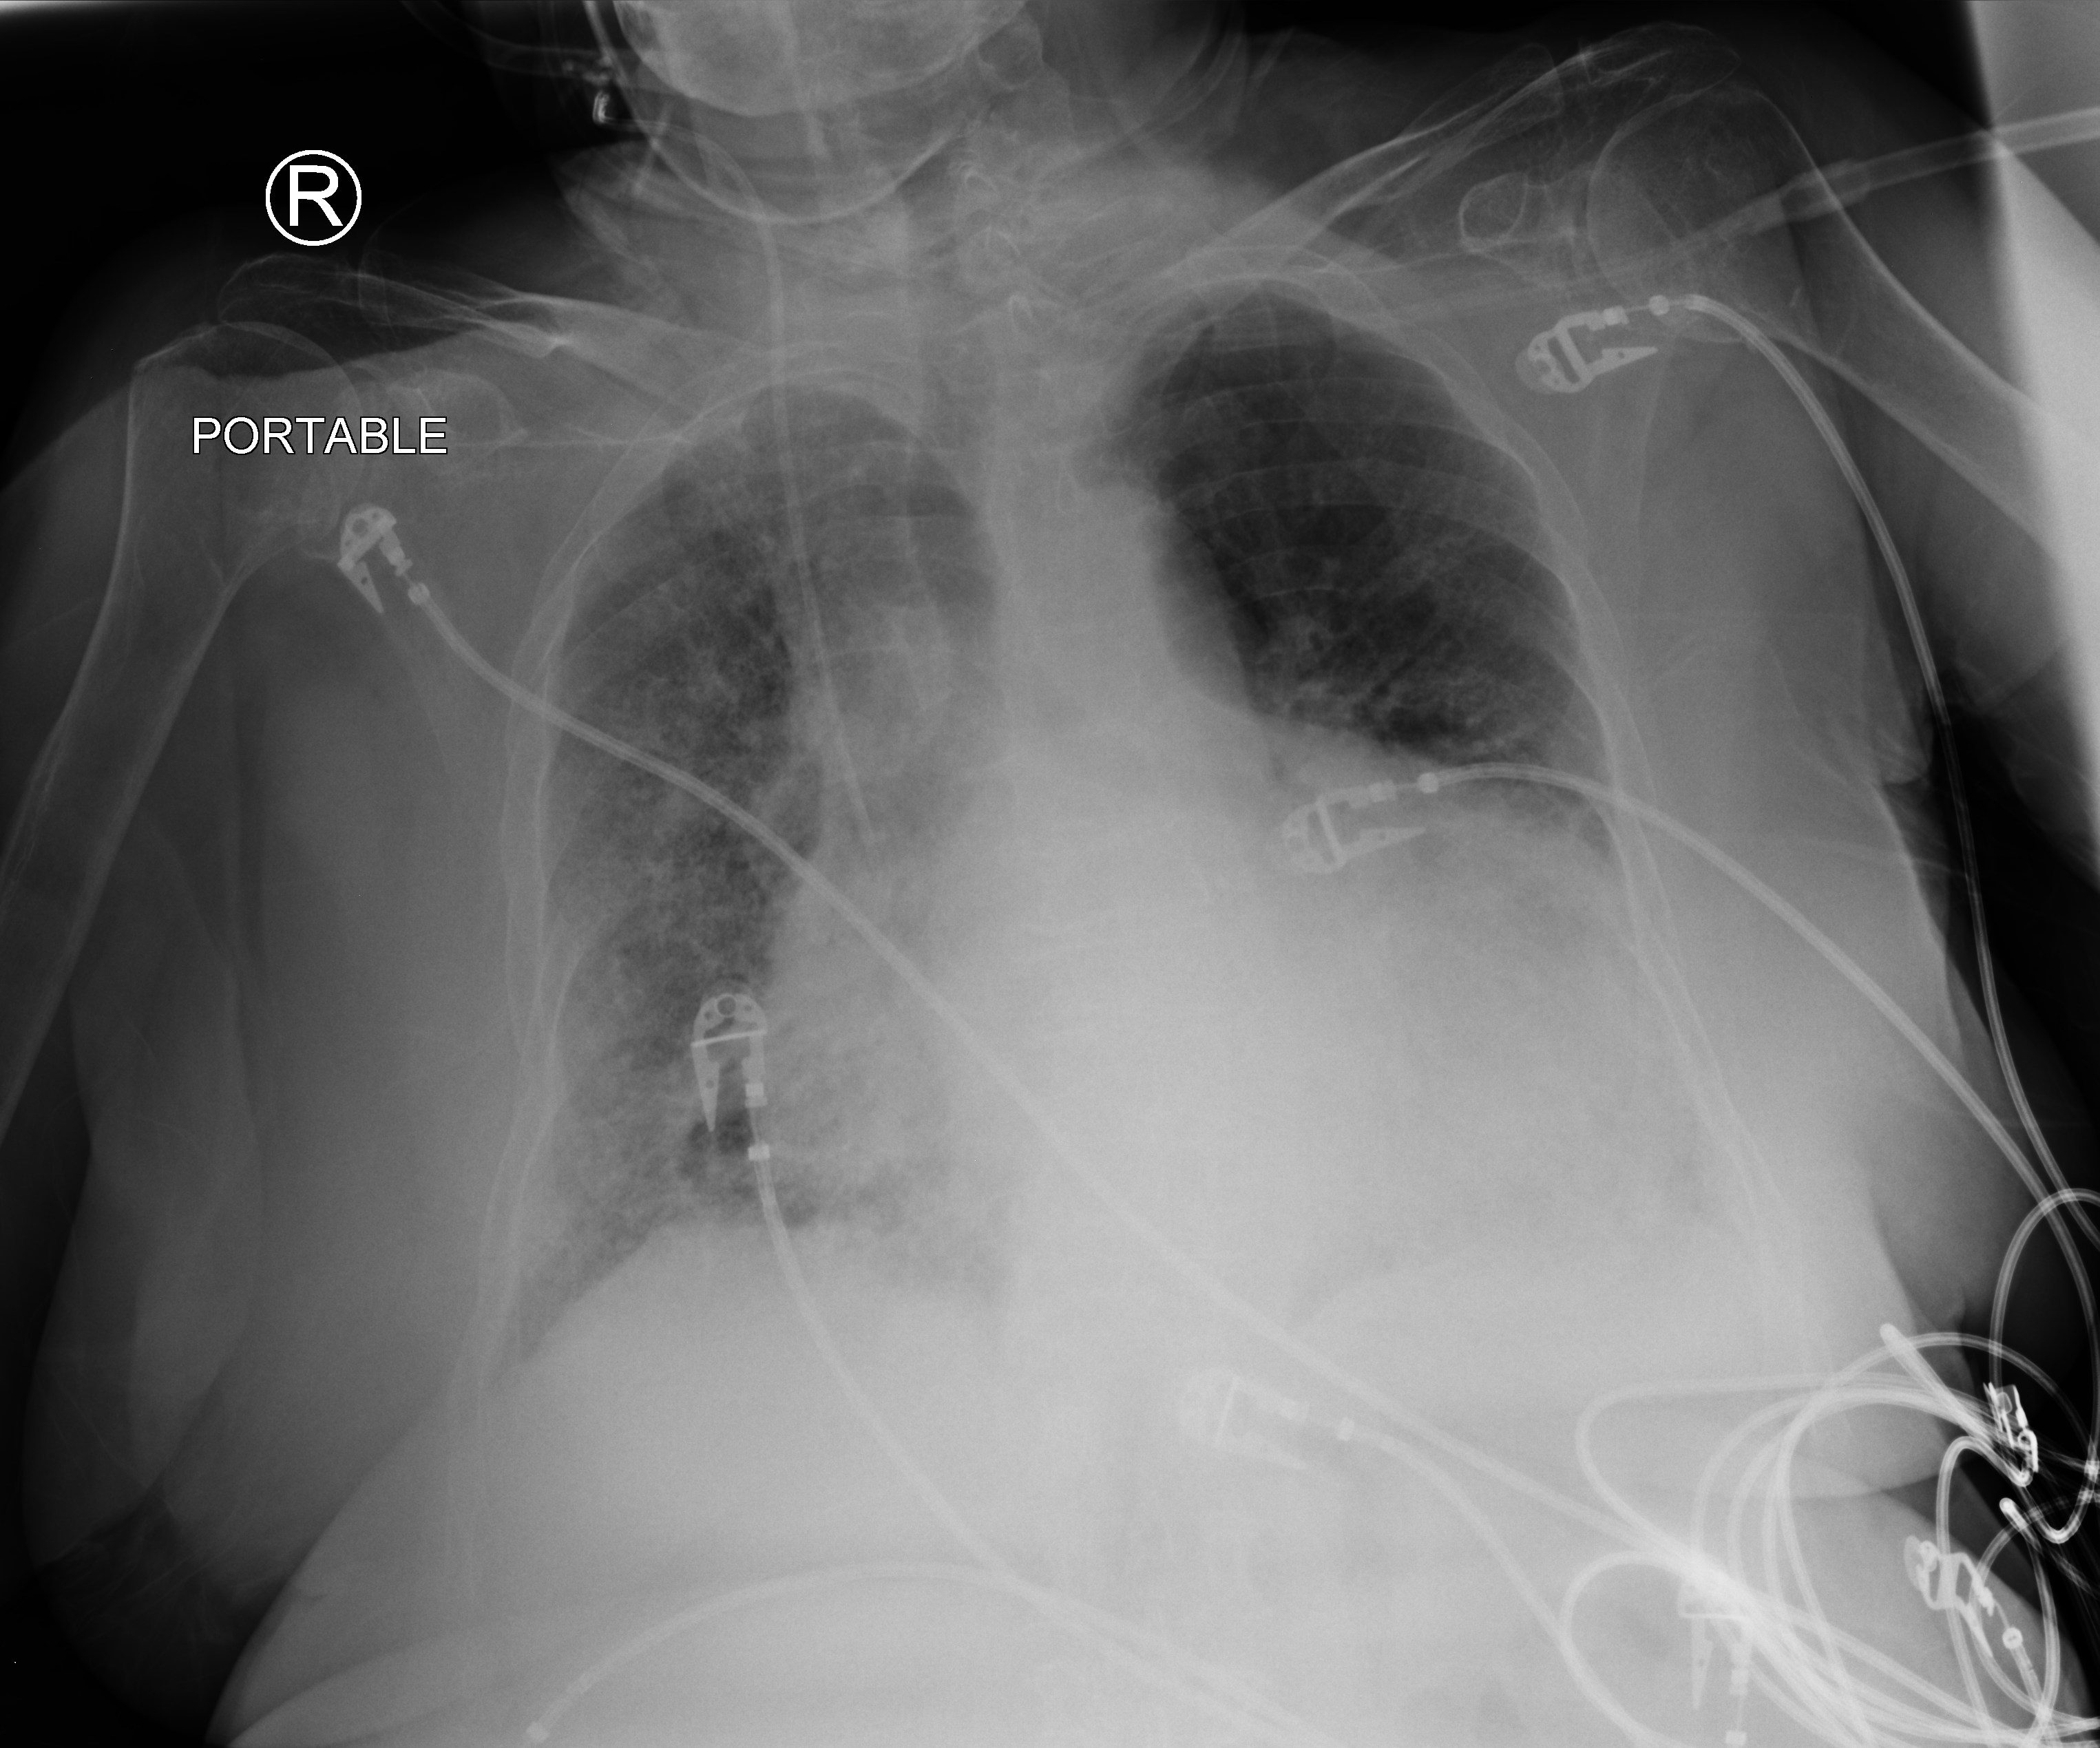
Portable chest radiograph; anteroposterior (AP) projection. Patient hospitalised with COVID-19; female, aged 75–90 years.
Admission-level facts for this patient (not findings on this image; timing relative to this image not recorded): admitted to intensive care during this hospital stay: no; mechanically ventilated during this hospital stay: no.